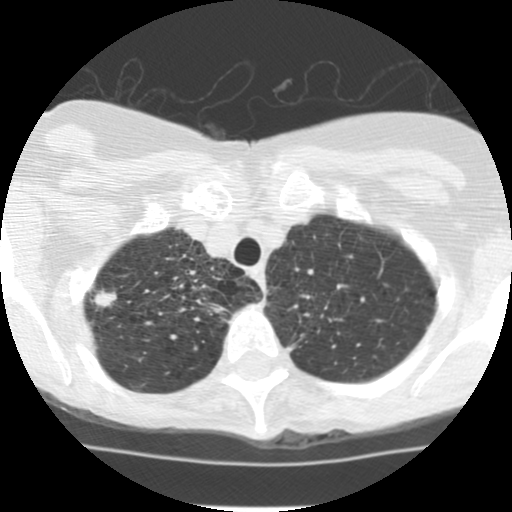
Low-dose screening chest CT, axial slice; baseline screening round; lung window (W 1500 / L -600 HU); standard (soft-tissue) reconstruction kernel (STANDARD); slice 24 of 135 in the series; 512 × 512 image matrix. Female, age 68 years at enrolment.
Lesion marked by an expert reader, box from (x=71, y=275) to (x=129, y=328) px. The screening reader recorded 2 non-calcified nodules or masses ≥4 mm on this exam; which of them this box marks is not recorded. Official screen result: positive, change unspecified: nodule(s) >= 4 mm or enlarging nodule(s), mass(es), or other non-specific abnormalities suspicious for lung cancer. Later outcome: lung cancer diagnosed 411 days after this screen (after the second annual screen) — large cell neuroendocrine carcinoma, right upper lobe, undifferentiated (G4), stage IB (AJCC 6th edition), 22 mm at pathology.